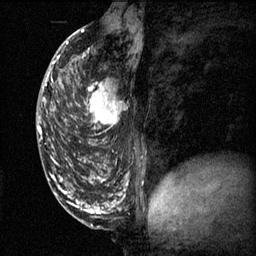
Breast MRI (dynamic contrast-enhanced), one sagittal slice. Slice 29 of 60 in the series (ordered by position). 3 images stored at this slice position (order not interpretable as contrast timing). 1.5 T. TE 4.2 ms, TR 11.1 ms. 256 × 256 image matrix, field of view 180 × 180 mm. Female patient, age 50 years.
Structures marked on this image (semi-automatically segmented with operator editing):
- analysis volume of interest (the breast-tissue region the enhancement analysis was run in; not a lesion): bounding box (x1, y1, x2, y2) in pixels: (68, 68, 133, 141)
- tumour enhancement mask (voxels above the 70 % enhancement threshold inside the analysis volume of interest): (68, 70, 126, 133)